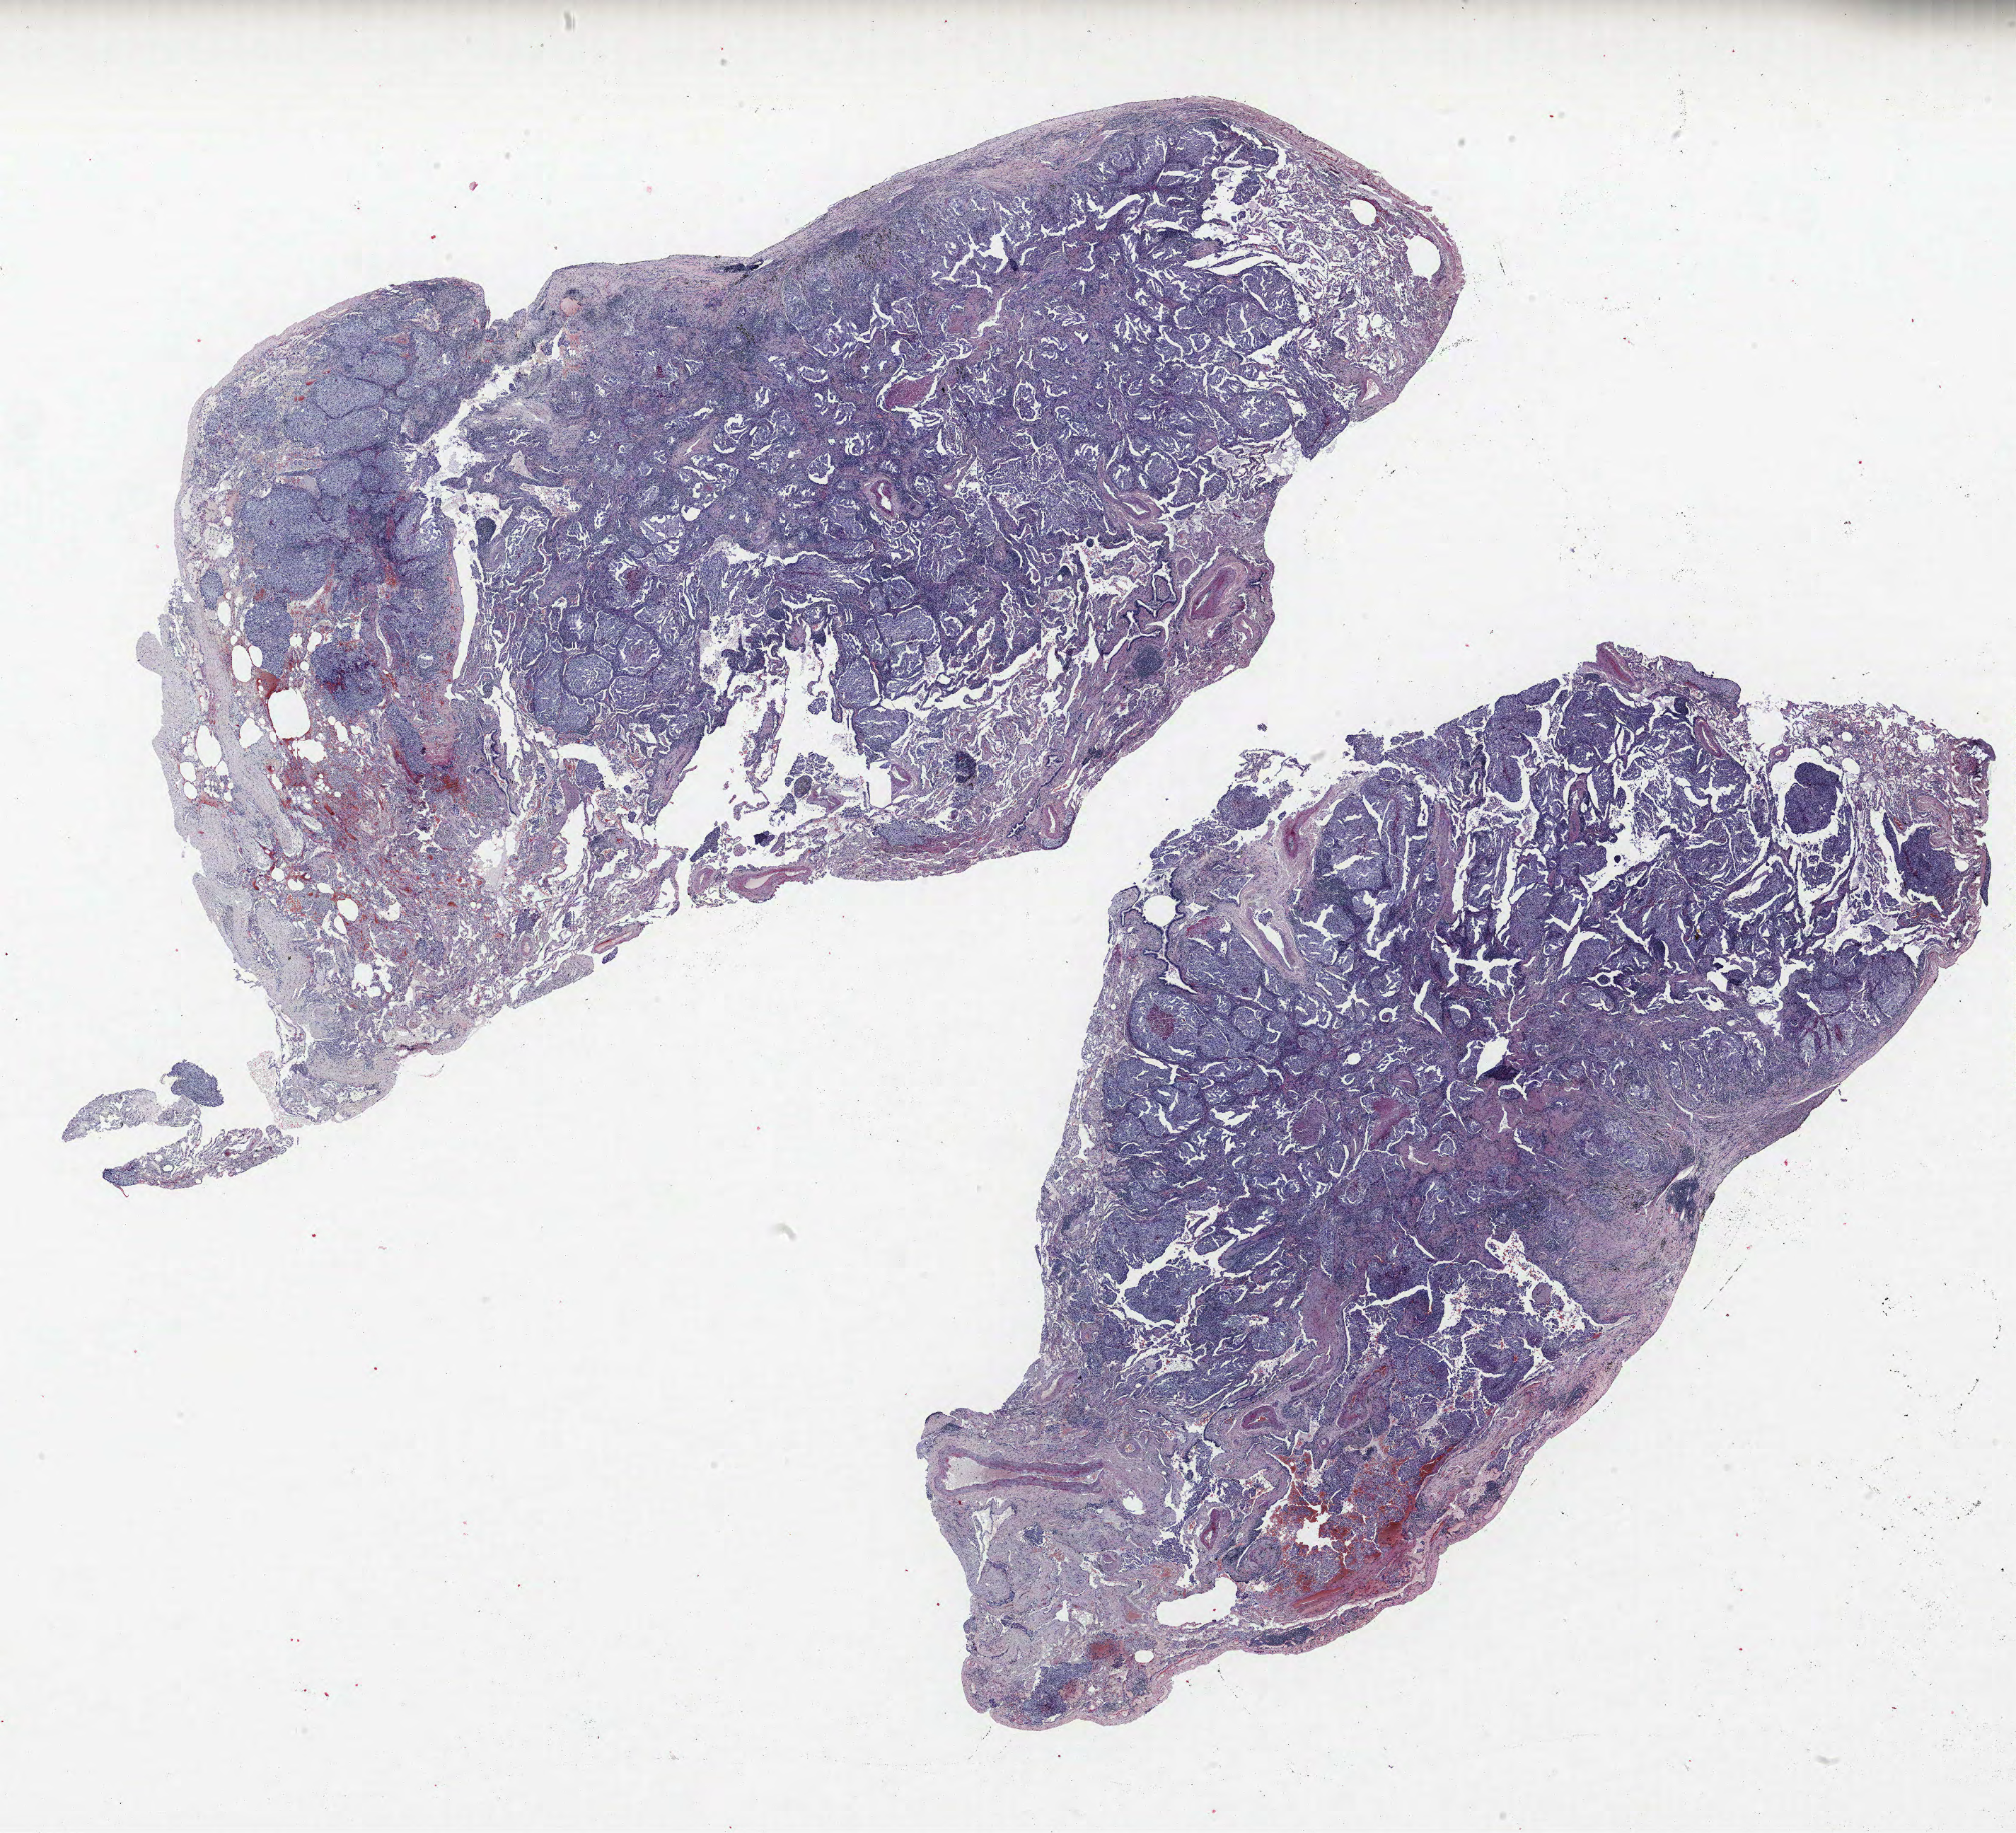
Whole-slide histology image, H&E, a low-resolution overview of the entire scanned area, about 22.8 x 20.7 mm (slide scanned at 40x). FFPE section. Lung tissue. Male, age 67 at enrolment. Former smoker at enrolment. Grade: moderately differentiated (G2).
• participant's lung-cancer diagnosis: Squamous cell carcinoma, NOS
• tumour size (pathology): 15 mm
• primary tumour location (clinical record): right lower lobe
• ICD-O-3 topography: lower lobe of lung (C34.3)
• stage (AJCC 6th edition): IB